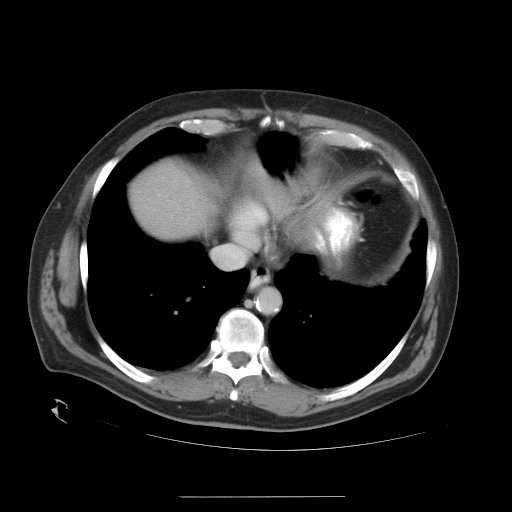
Contrast-enhanced abdominal CT, one axial slice. Reconstruction kernel STANDARD. 120 kVp. Intravenous contrast given. Soft-tissue window (W 400 / L 40 HU). 7.5 mm slice thickness. 512 × 512 image matrix, field of view 450 × 450 mm. Male patient, age 67 years. Case-level facts recorded for this patient, not image findings: diagnosis: colorectal cancer liver metastases, imaged before liver resection; multiple liver metastases: no; largest metastasis: 2.3 cm; chemotherapy before resection: no.
Structures marked on this image (outlined manually by an expert reader):
- liver: bounding box [x1, y1, x2, y2] px = [132, 165, 203, 238]
- planned liver remnant (the part of the liver to remain after resection): [131, 165, 203, 238]